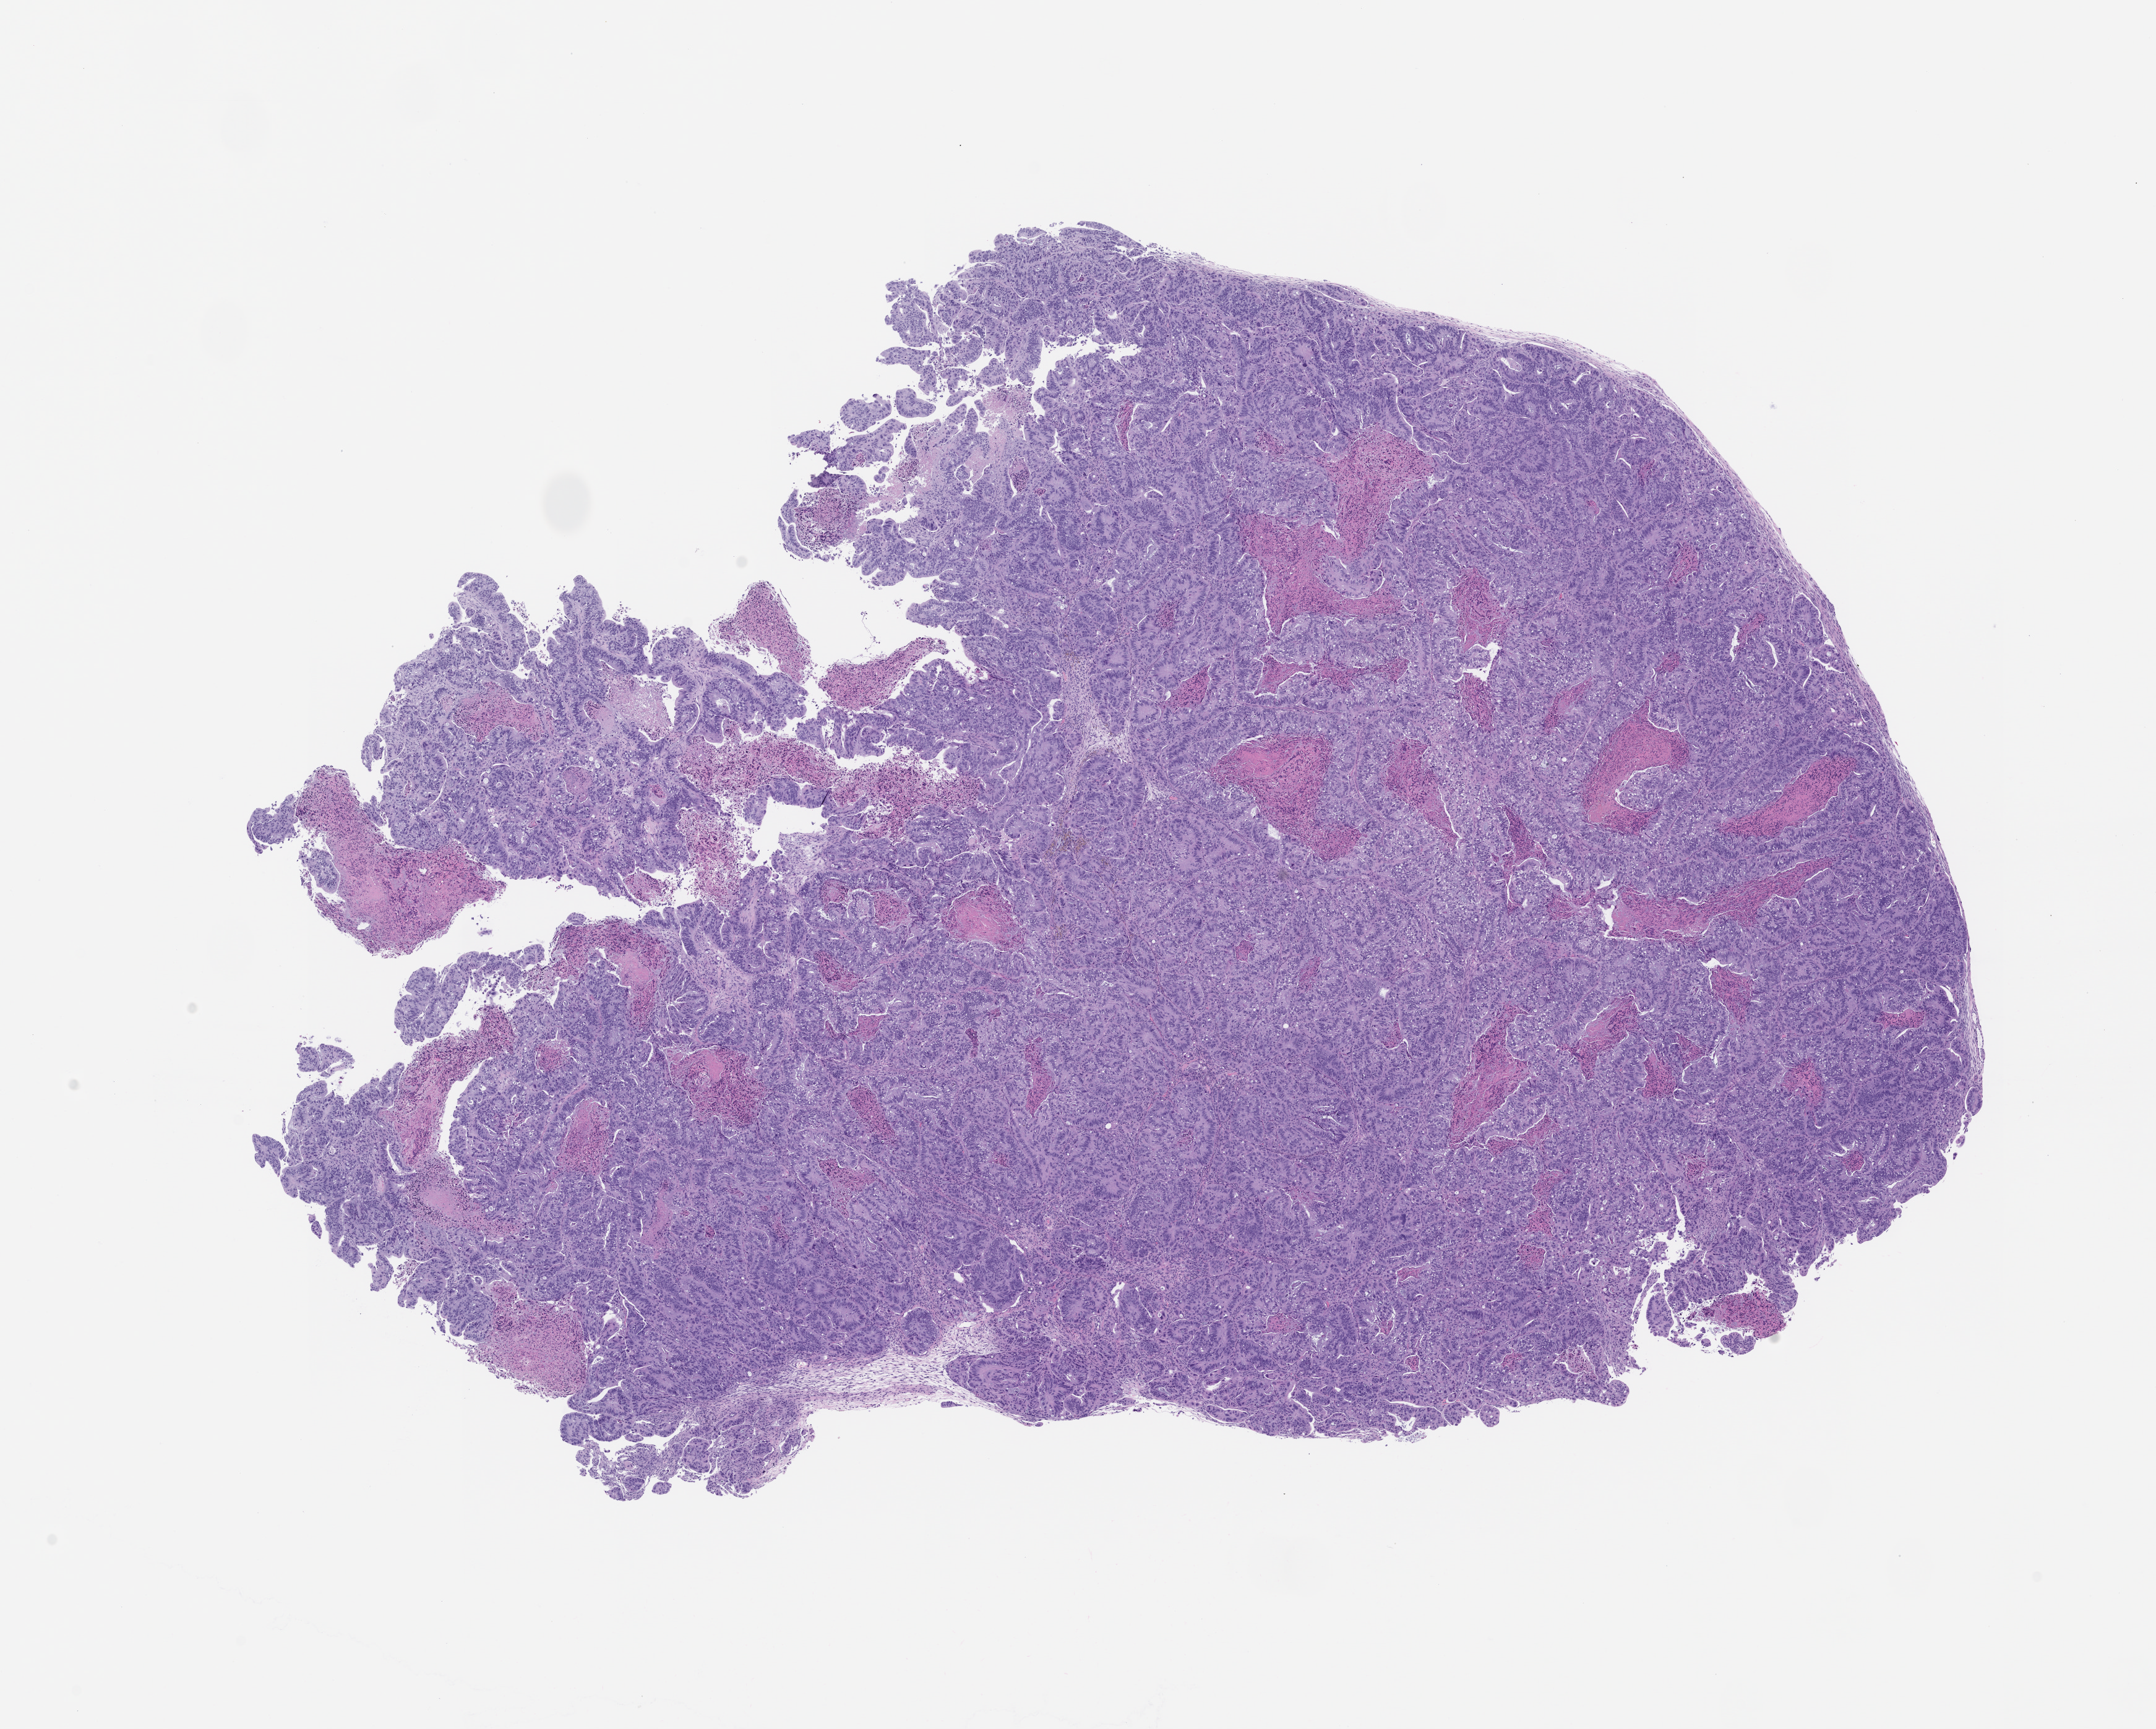
Whole-slide image, haematoxylin and eosin: patient-derived xenograft (human tumor grown in a mouse), passage 0 — whole scanned area (about 14.0 x 11.2 mm) shown as a low-resolution overview. Formalin-fixed, paraffin-embedded (FFPE) tissue. Originating tumor site category: colon.
Originating patient diagnosis: Colon Adenocarcinoma.